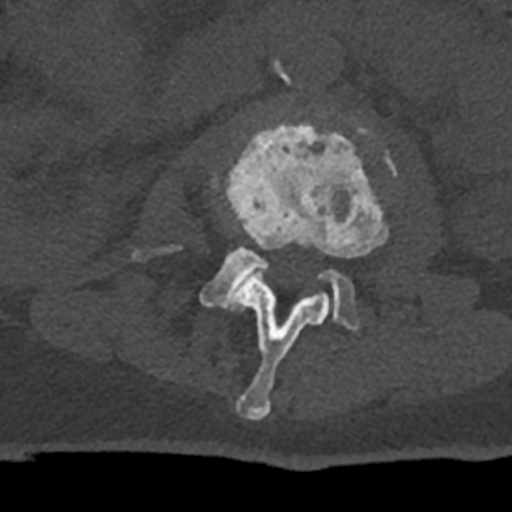
CT including the spine, one axial slice; slice 354 of 797 in the series (ordered by position); bone window (W 1800 / L 400 HU); 0.5 mm slice thickness; 512 × 512 image matrix, field of view 160 × 160 mm. Patient: male, 74 years. From the clinical record (not read from this slice): primary cancer: renal.
Outlined on this slice (semi-automatic segmentation, software-assisted and operator-edited):
- L2 vertebra: bounding box (x1, y1, x2, y2) in pixels: (212, 120, 389, 420)
- L3 vertebra: (132, 157, 385, 330)